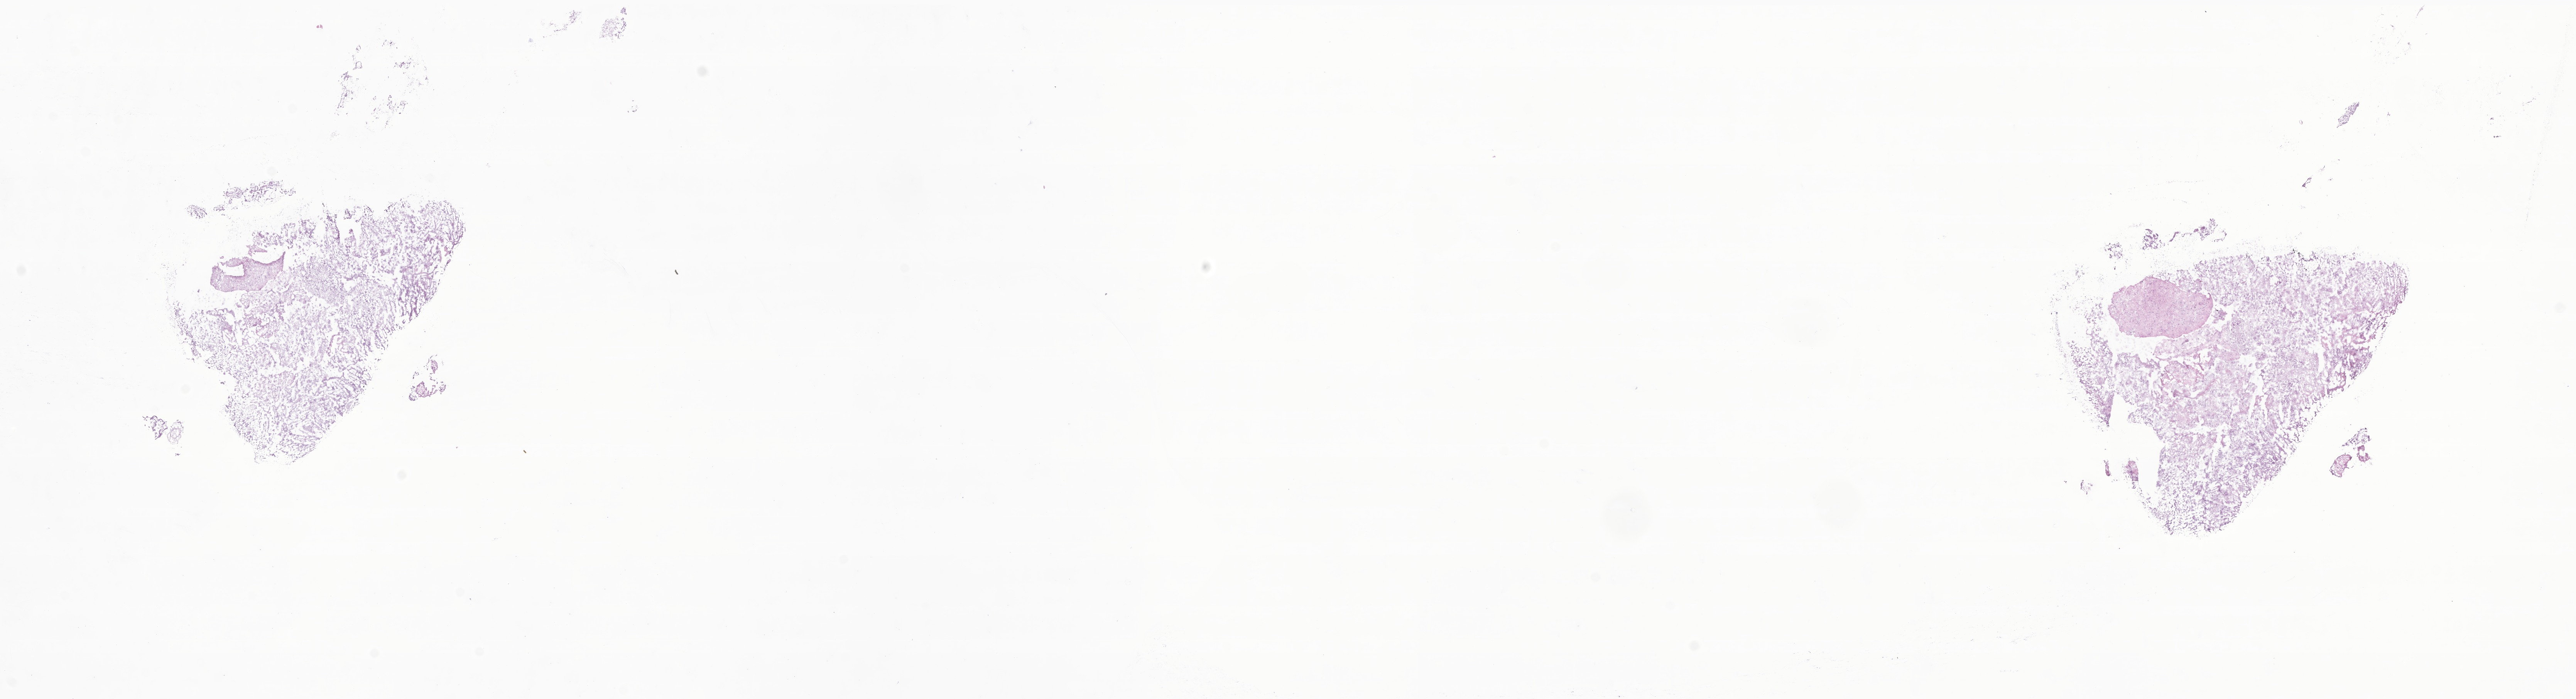
H&E whole-slide image of tumor tissue from the cerebral ventricle — a low-resolution overview of the entire scanned area, about 28.1 x 7.6 mm; cryosection (OCT / tissue freezing medium). Patient: male, age 196 months (16 years 4 months).
Diagnosis (ICD-O-3 morphology term): Central neurocytoma.